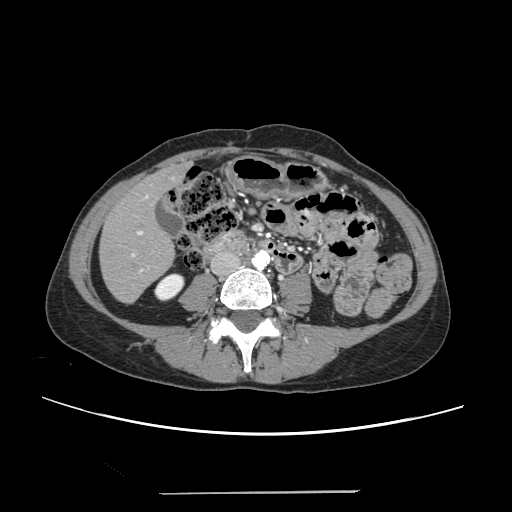
Contrast-enhanced abdominal CT, one axial slice; slice 63 of 240 in the series (ordered by position); 120 kVp; intravenous contrast given; soft-tissue window (W 400 / L 40 HU); 512 × 512 image matrix. Female patient, age 60 years. Case-level facts recorded for this patient, not image findings: diagnosis: colorectal cancer liver metastases, imaged before liver resection; multiple liver metastases: no; largest metastasis: 1.5 cm; disease in both lobes: no.
Structures marked on this image (manually delineated by an expert):
- liver: bounding box [x1, y1, x2, y2] px = [101, 167, 184, 302]
- planned liver remnant (the part of the liver to remain after resection): [101, 172, 174, 302]
- portal vein (with intrahepatic branches): [131, 195, 149, 273]